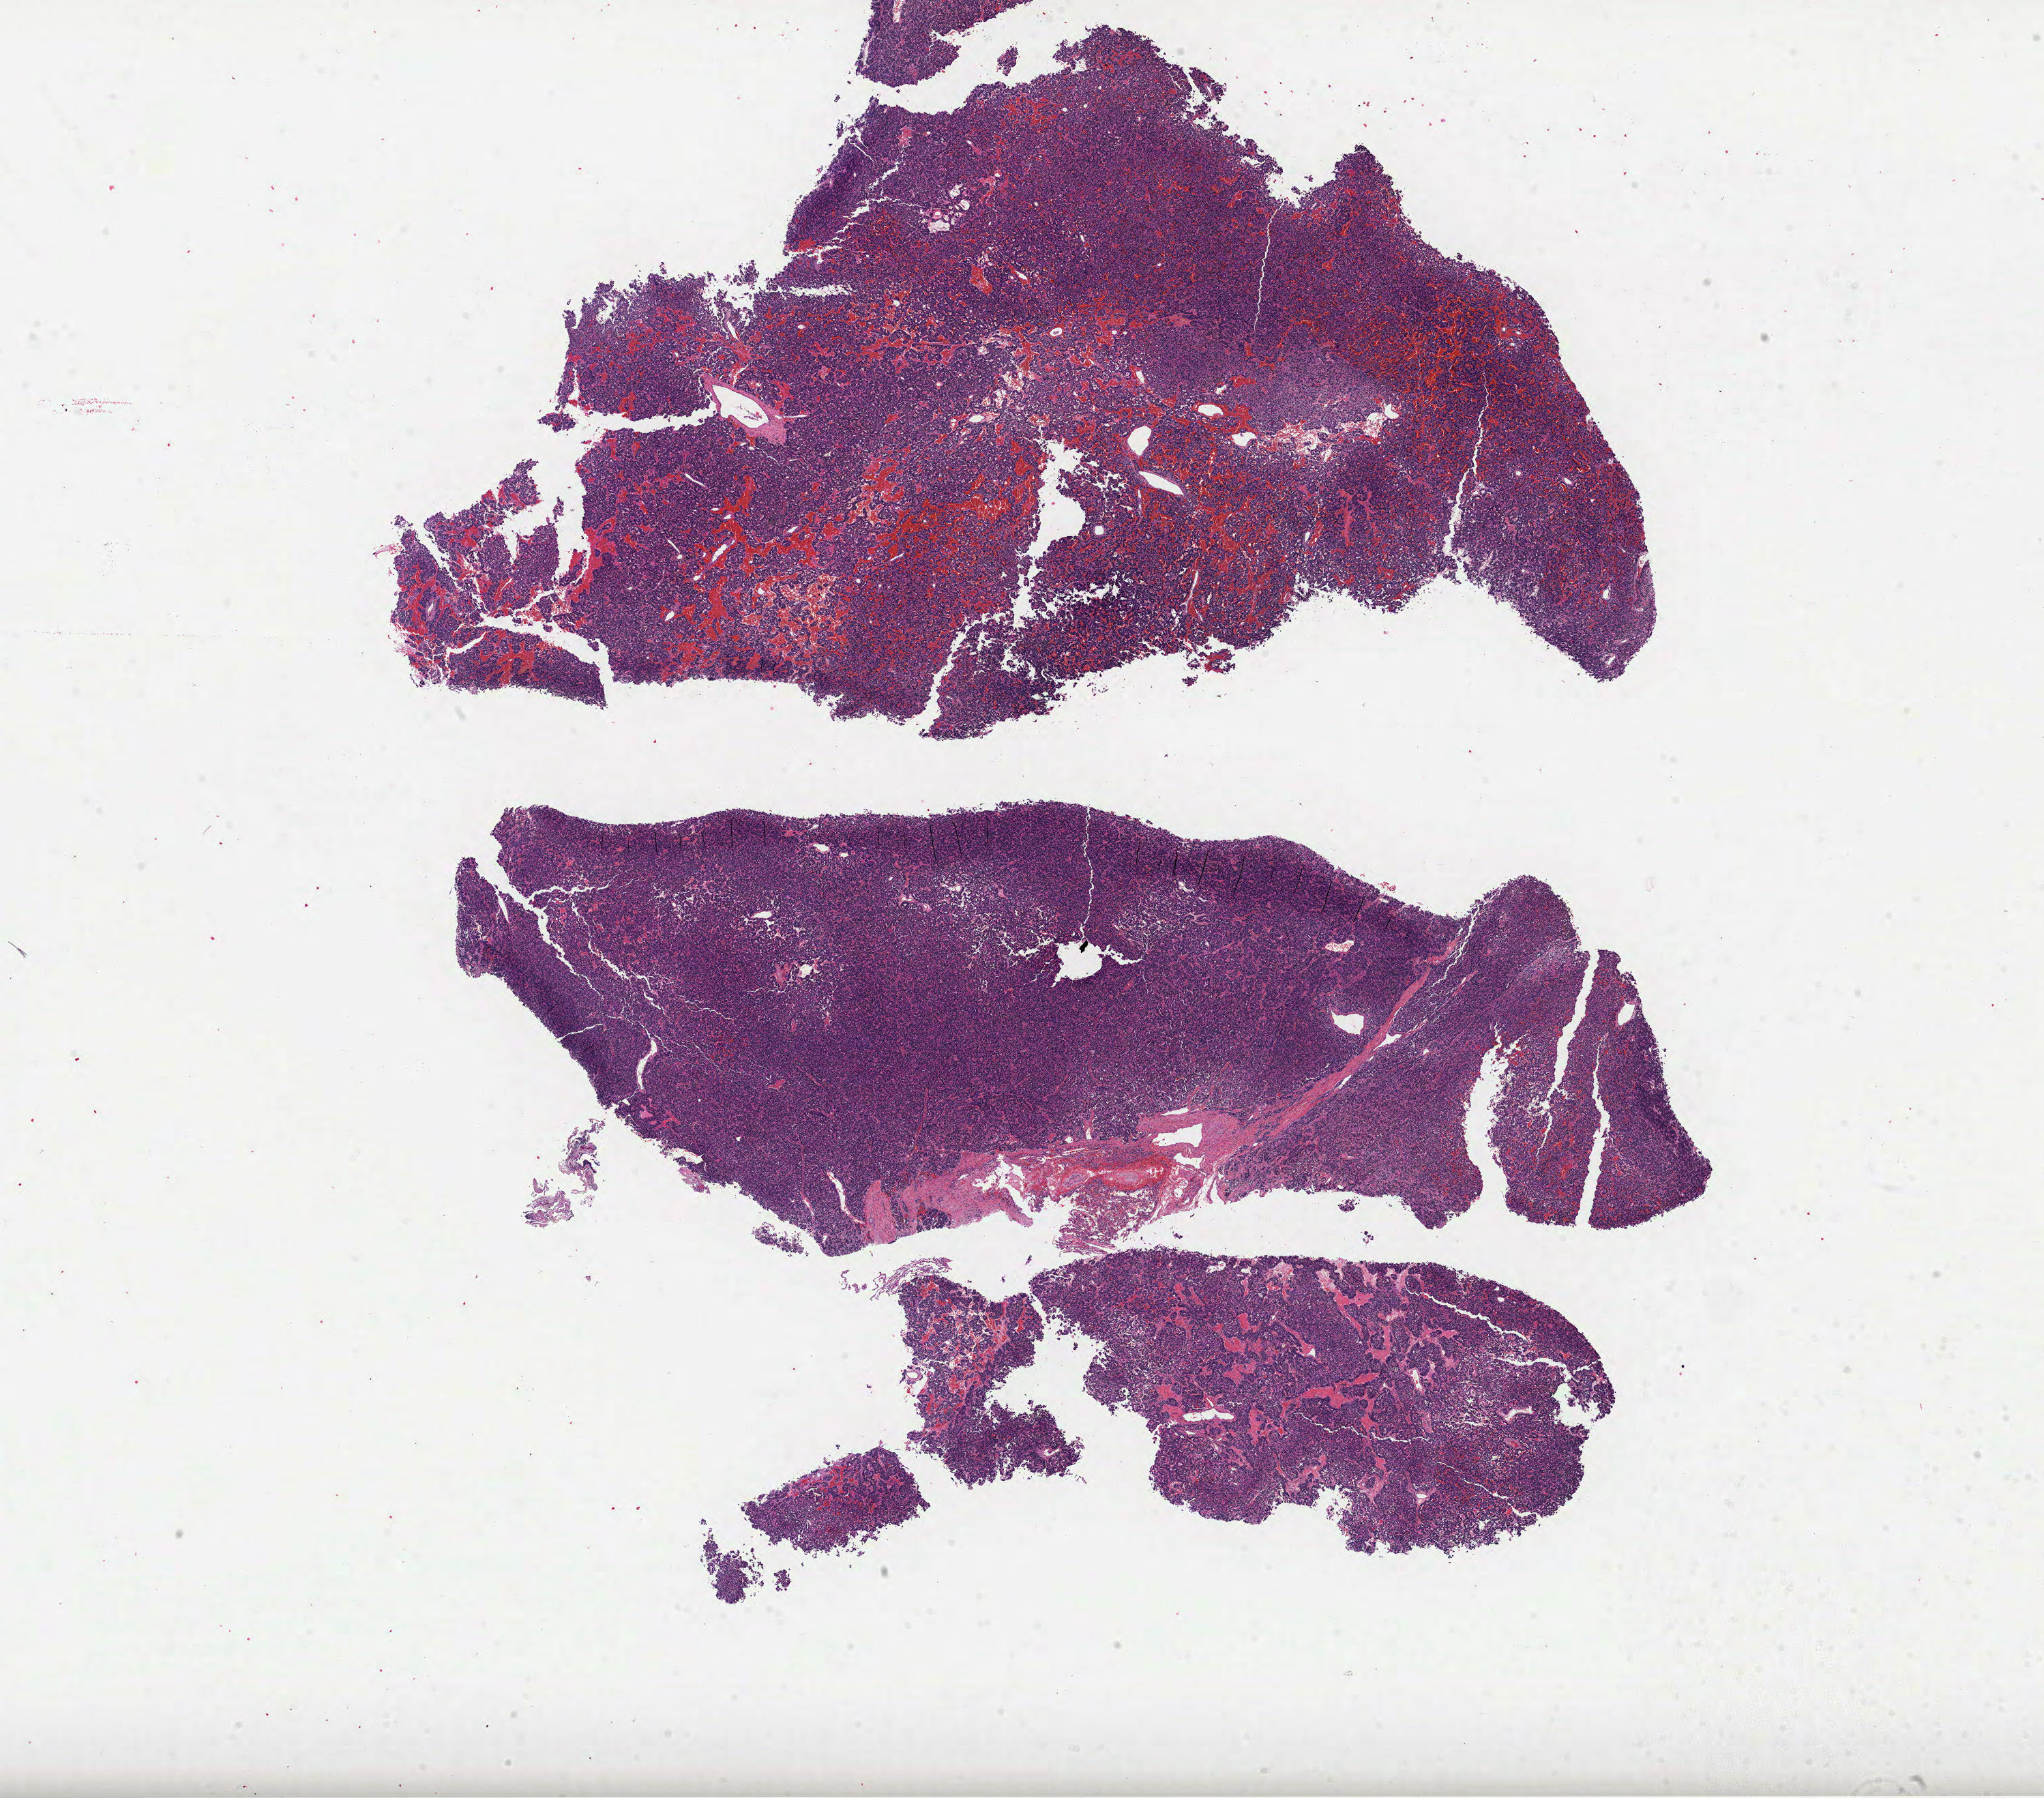
H&E whole-slide image, whole scanned area (about 24.2 x 21.3 mm) shown as a low-resolution overview; FFPE section; primary tumour sample from the lung. Female, age 52 years at initial diagnosis.
Histologic diagnosis: Squamous cell carcinoma, NOS. AJCC pathologic stage: IA. TNM: T1b N0 M0. Laterality: right.